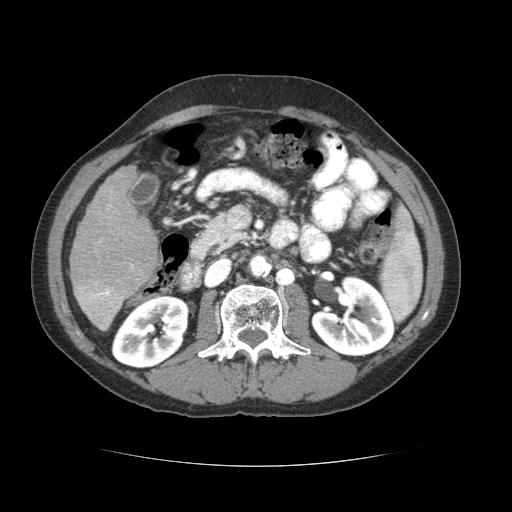
Contrast-enhanced abdominal CT (liver protocol), one axial slice; position 24 of 69 along the scan axis; reconstruction kernel STANDARD; 120 kVp; soft-tissue window (W 400 / L 40 HU); 512 × 512 image matrix. From the clinical record (not read from this slice): diagnosis: hepatocellular carcinoma (patient treated with transarterial chemoembolisation; whether this scan precedes or follows treatment is not stated here); TNM stage (as recorded): Stage-II; Child-Pugh class: B; tumour nodularity: multinodular.
Annotated regions visible in this slice (semi-automatically segmented with operator editing):
- liver parenchyma outside the tumour (the mass and vessels are separate outlines, so this box may not span the whole liver): bounding box [x1, y1, x2, y2] px = [70, 166, 158, 330]
- liver vessels: [78, 204, 134, 328]